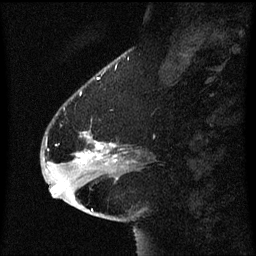
Breast MRI (dynamic contrast-enhanced), one sagittal slice; position 19 of 60 along the scan axis; dynamic contrast-enhanced series, image 2 of 3 at this slice position (ordered by acquisition); 1.5 T; TE 4.2 ms, TR 8.4 ms; 2 mm slice thickness; 256 × 256 image matrix, field of view 200 × 200 mm. Patient: female, 54 years. Case-level facts recorded for this patient, not image findings: setting: breast cancer imaged before/during neoadjuvant chemotherapy; receptor status: HR-positive, HER2-negative.
Annotated regions visible in this slice (semi-automatically segmented with operator editing):
- analysis volume of interest (the breast-tissue region the enhancement analysis was run in; not a lesion): bounding box [x1, y1, x2, y2] px = [46, 108, 123, 171]
- tumour enhancement mask (voxels above the 70 % enhancement threshold inside the analysis volume of interest): [78, 142, 118, 161]